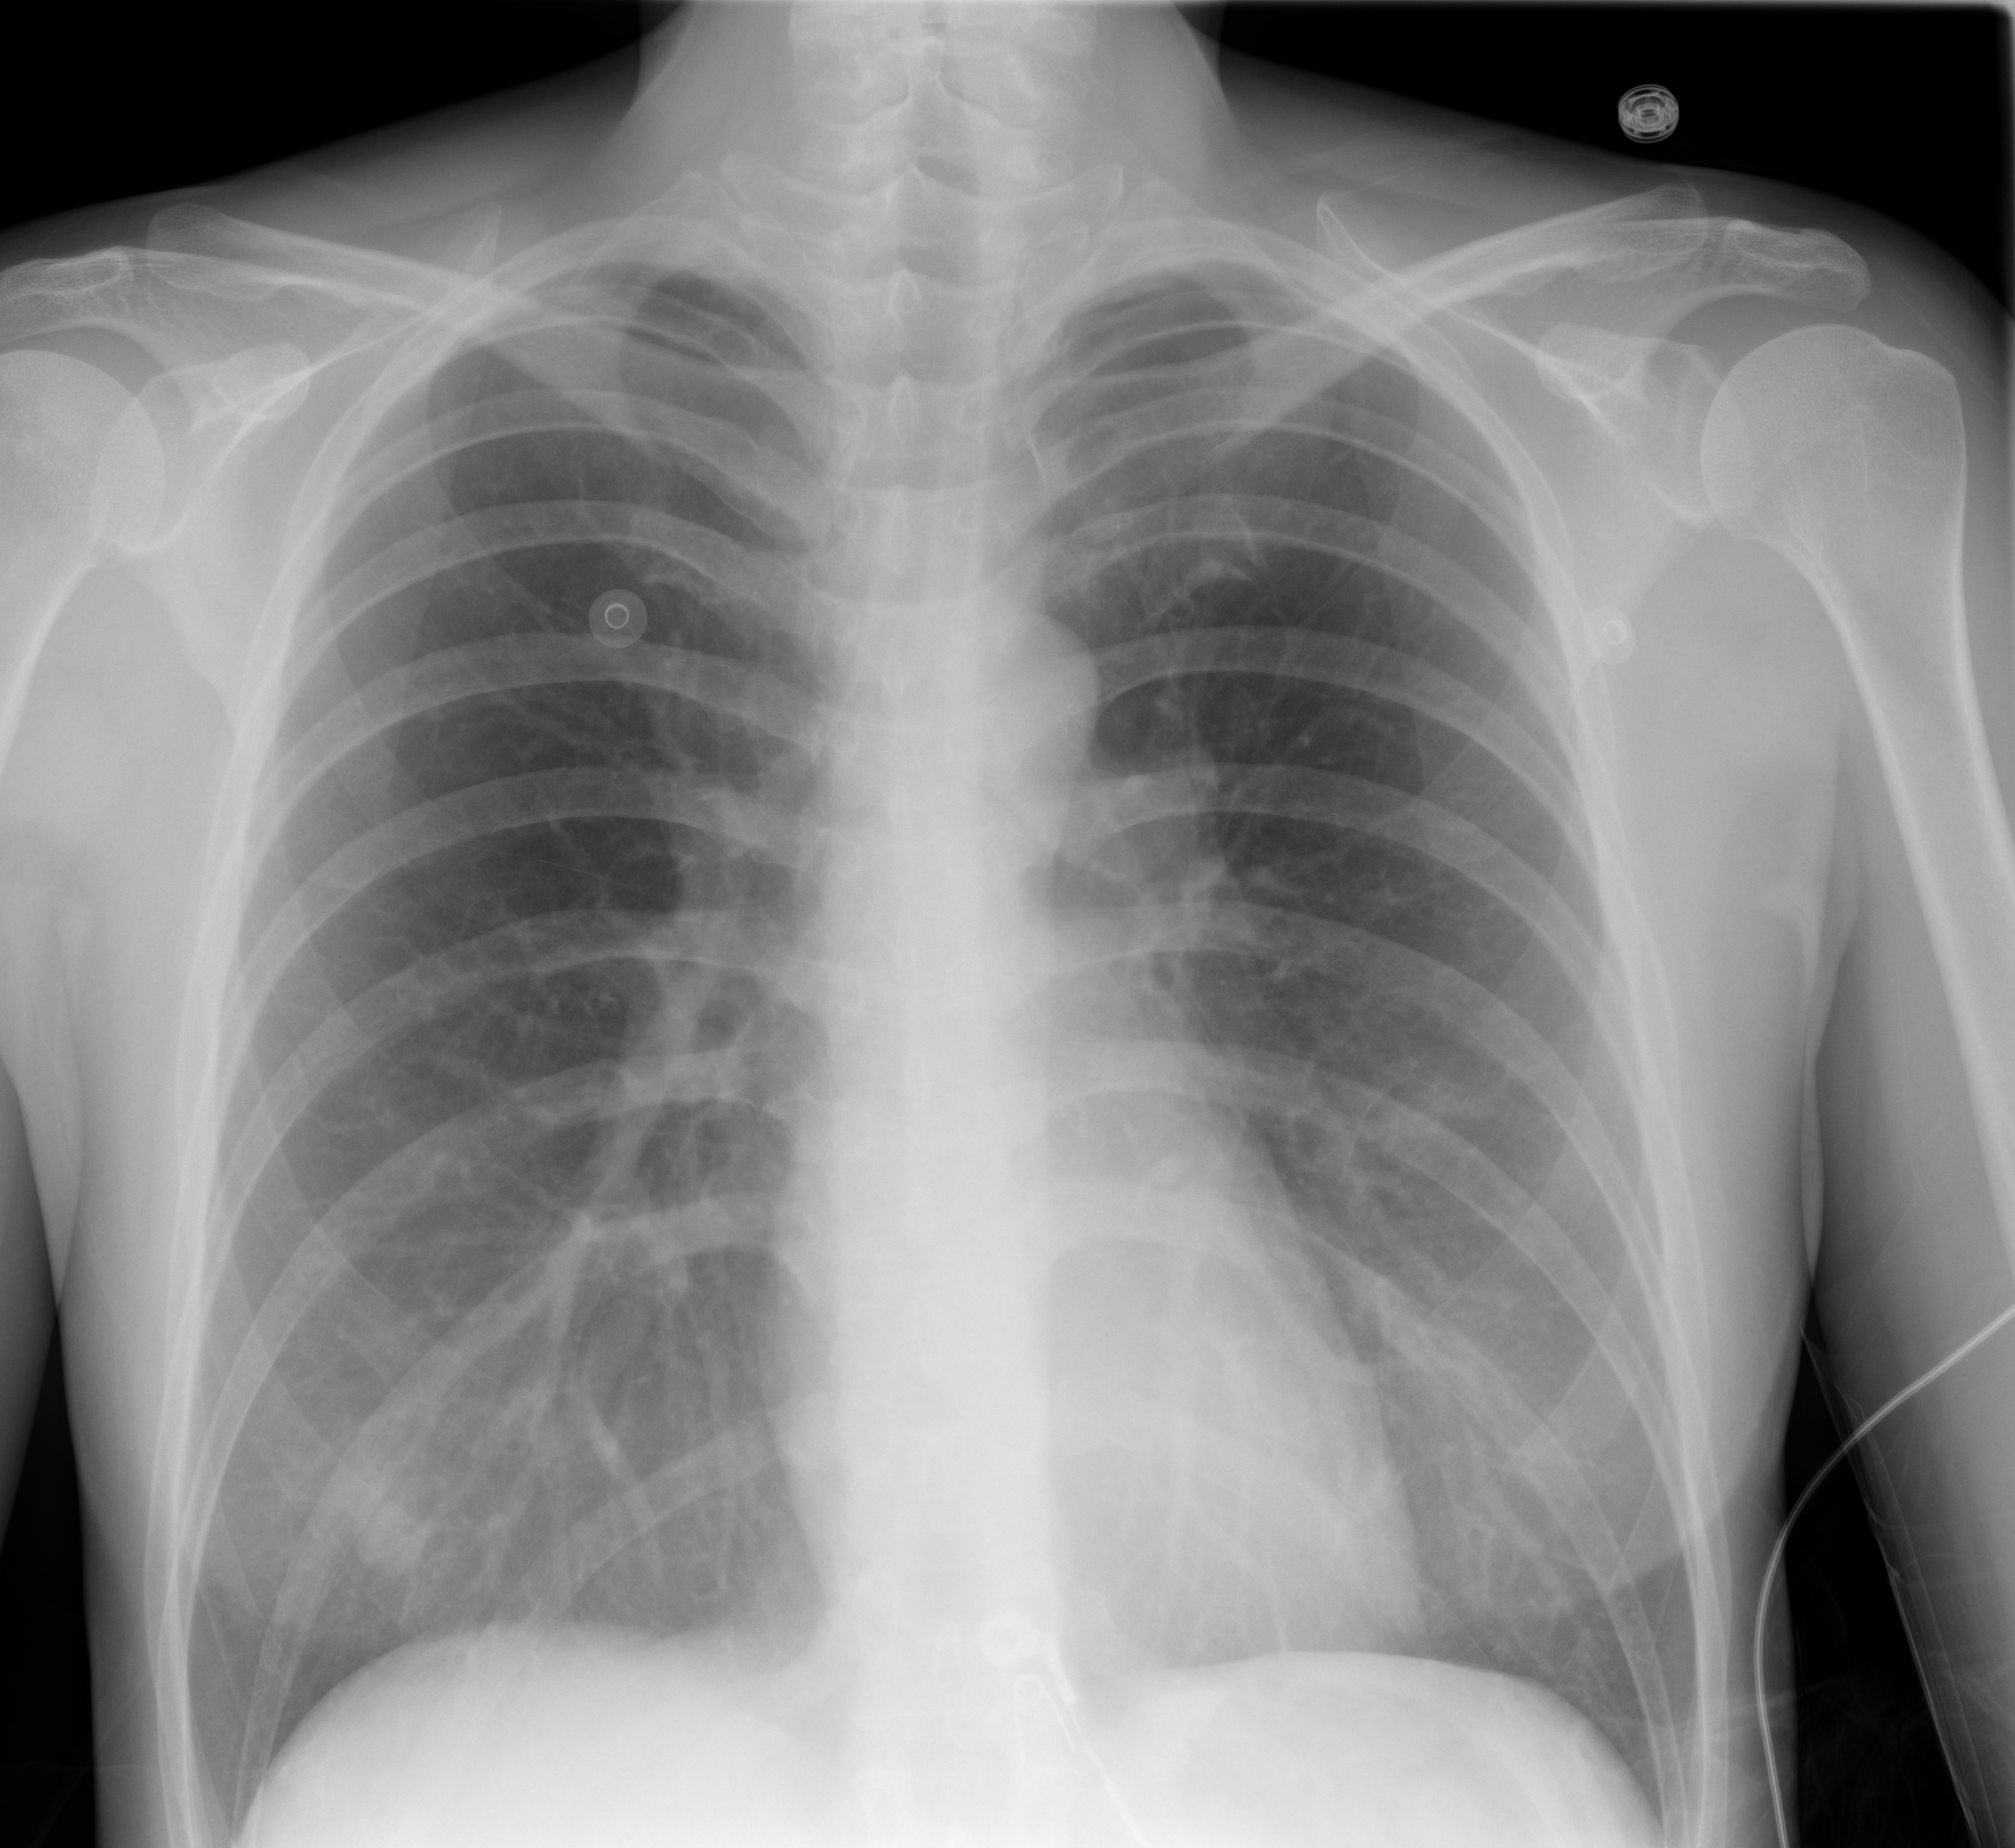
Chest X-ray (portable), AP projection. Female patient, age 41 years; imaged 4 days after the COVID-19 diagnosis.
Key findings recorded by the radiologist: The lungs are clear and well inflated.